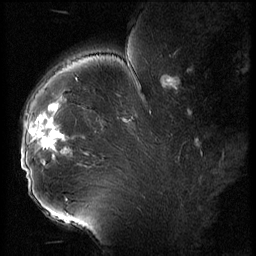
Breast MRI (dynamic contrast-enhanced), one sagittal slice; slice 41 of 56 in the series (ordered by position); 3 images stored at this slice position (order not interpretable as contrast timing); 1.5 T; TE 4.2 ms, TR 9 ms; 2.5 mm slice thickness; 256 × 256 image matrix, field of view 180 × 180 mm. Female patient, age 43 years. Case-level facts recorded for this patient, not image findings: setting: breast cancer imaged before/during neoadjuvant chemotherapy; receptor status: HER2-positive.
Annotated regions visible in this slice (semi-automatic segmentation, software-assisted and operator-edited):
- analysis volume of interest (the breast-tissue region the enhancement analysis was run in; not a lesion): bounding box [x1, y1, x2, y2] px = [21, 92, 74, 211]
- tumour enhancement mask (voxels above the 140 % enhancement threshold inside the analysis volume of interest): [31, 127, 65, 149]